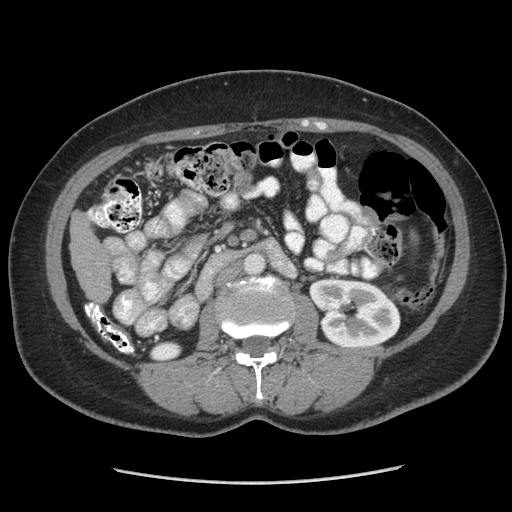
Contrast-enhanced abdominal CT (liver protocol), one axial slice. Position 115 of 185 along the scan axis. Reconstruction kernel STANDARD. Soft-tissue window (W 400 / L 40 HU). 2.5 mm slice thickness. 512 × 512 image matrix, field of view 360 × 360 mm. Case-level facts recorded for this patient, not image findings: diagnosis: hepatocellular carcinoma (patient treated with transarterial chemoembolisation; whether this scan precedes or follows treatment is not stated here); TNM stage (as recorded): Stage-I; Child-Pugh class: A; tumour differentiation: poorly differentiated.
Outlined on this slice (semi-automatically segmented with operator editing):
- liver parenchyma outside the tumour (the mass and vessels are separate outlines, so this box may not span the whole liver): bounding box (x1, y1, x2, y2) in pixels: (70, 211, 110, 302)